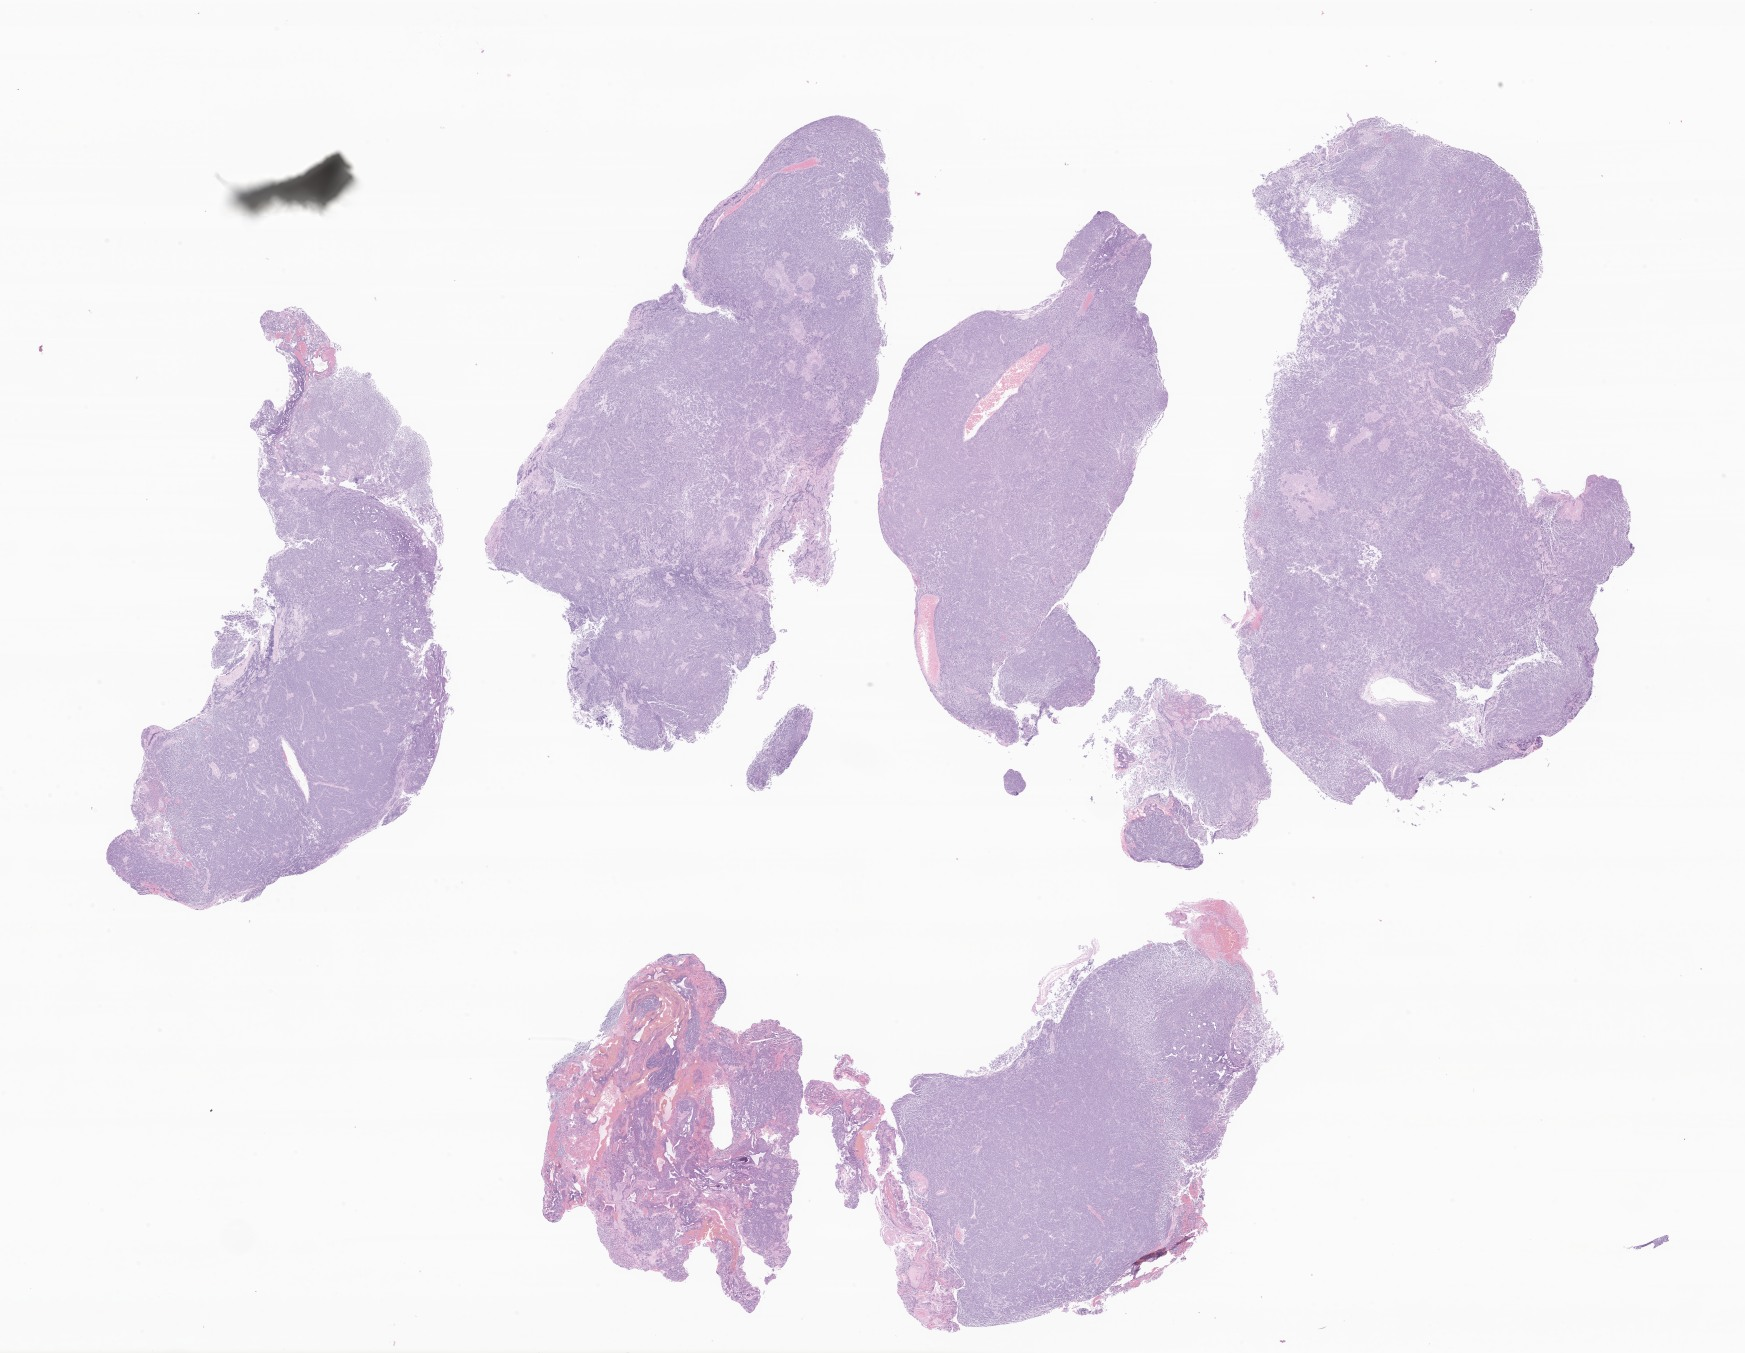
Whole-slide image, haematoxylin and eosin stain of tumor tissue from the brain — low-resolution overview of the scanned area, about 29.4 x 22.8 mm, FFPE section. Patient male; age 56 months (4 years 8 months).
Recorded diagnosis: Medulloblastoma, NOS.